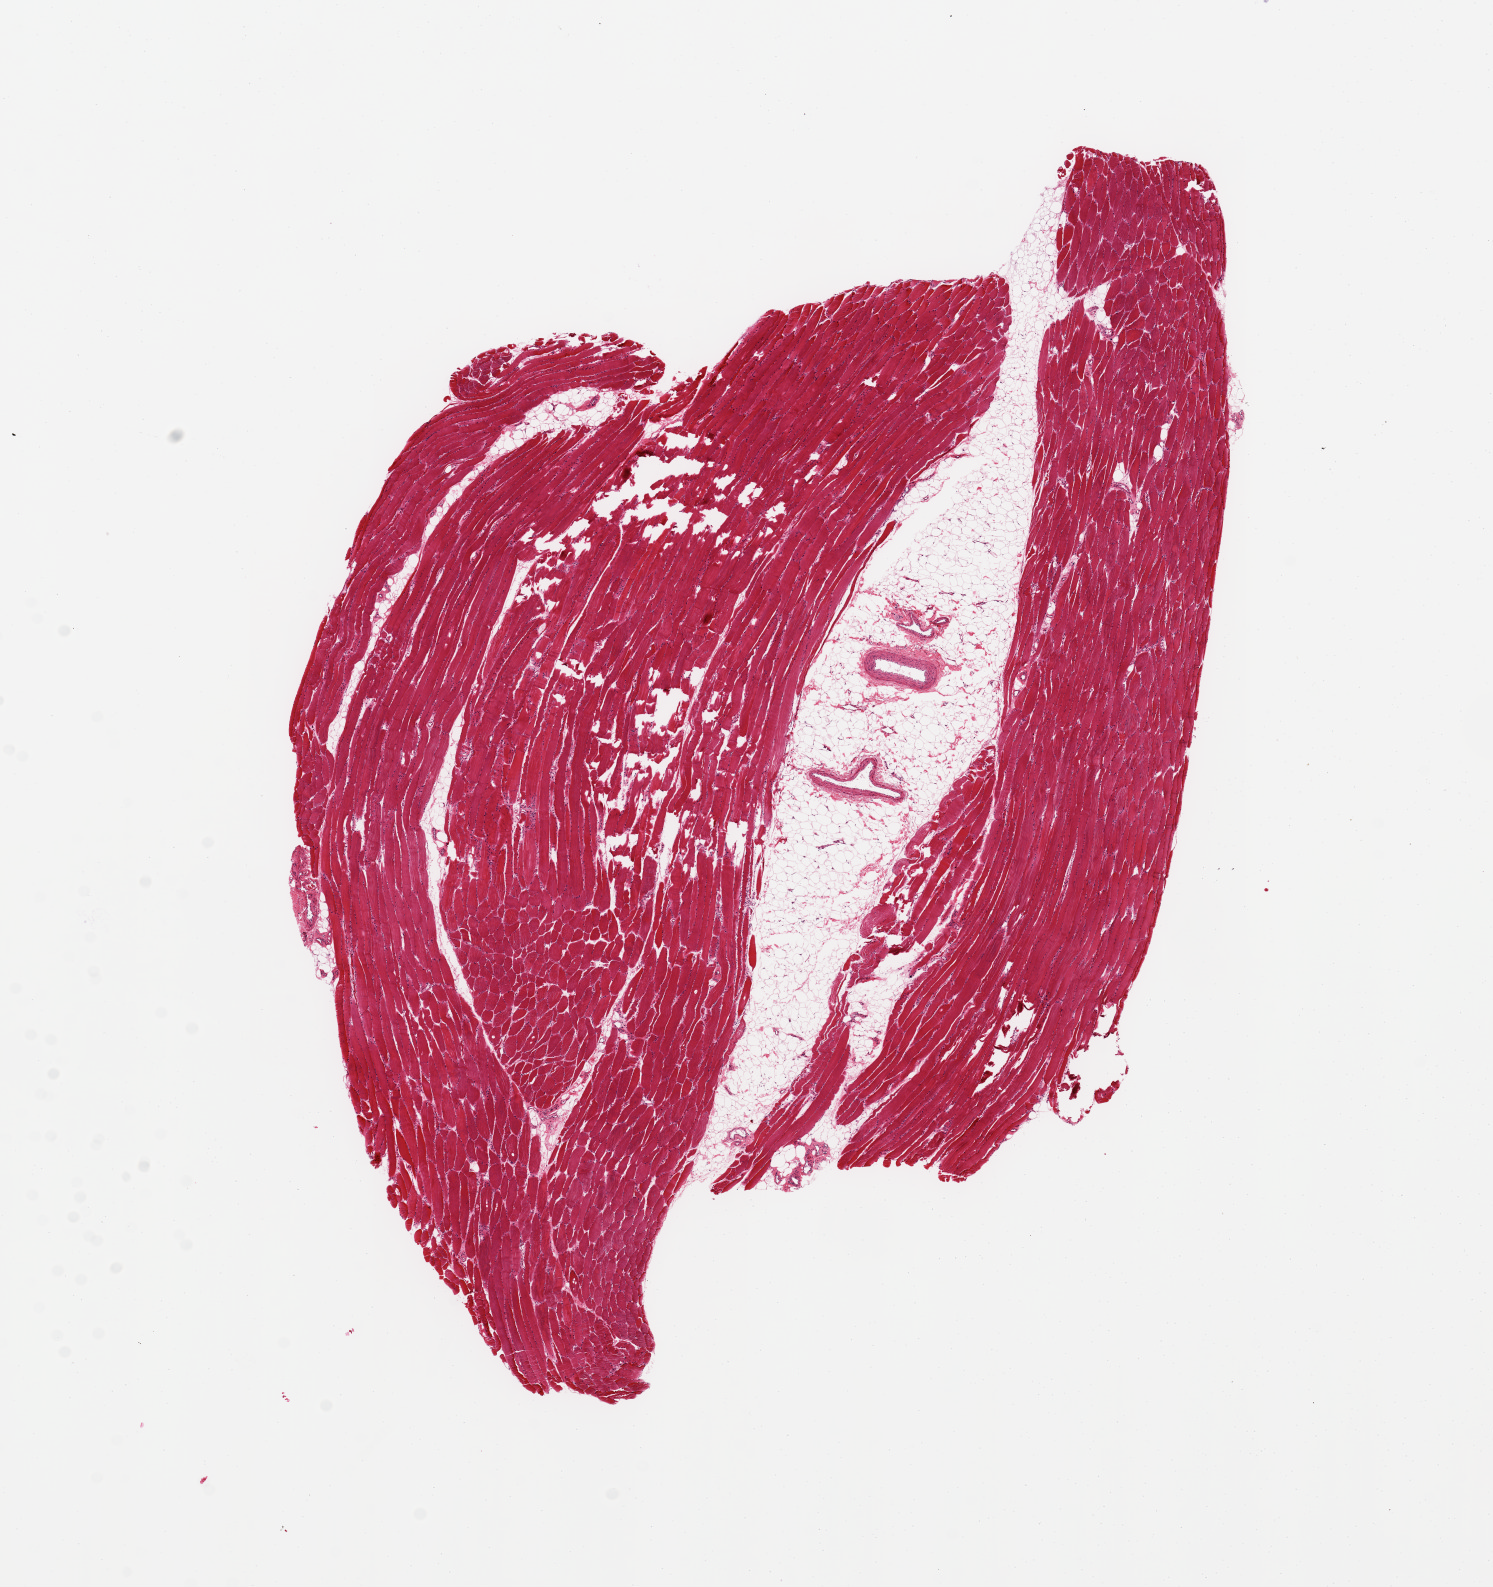
Digitized H&E-stained section, shown as a low-resolution overview of the whole scanned area (about 11.8 x 12.6 mm, from a 20x scan), PAXgene-fixed paraffin-embedded (PFPE) section, sampled site (target tissue): skeletal muscle, donor tissue sample. Donor: male.
• review note (as recorded): 9x7mm. Central 7.7x1.4mm wedge of adipose tissue???focal areas of poor fixation